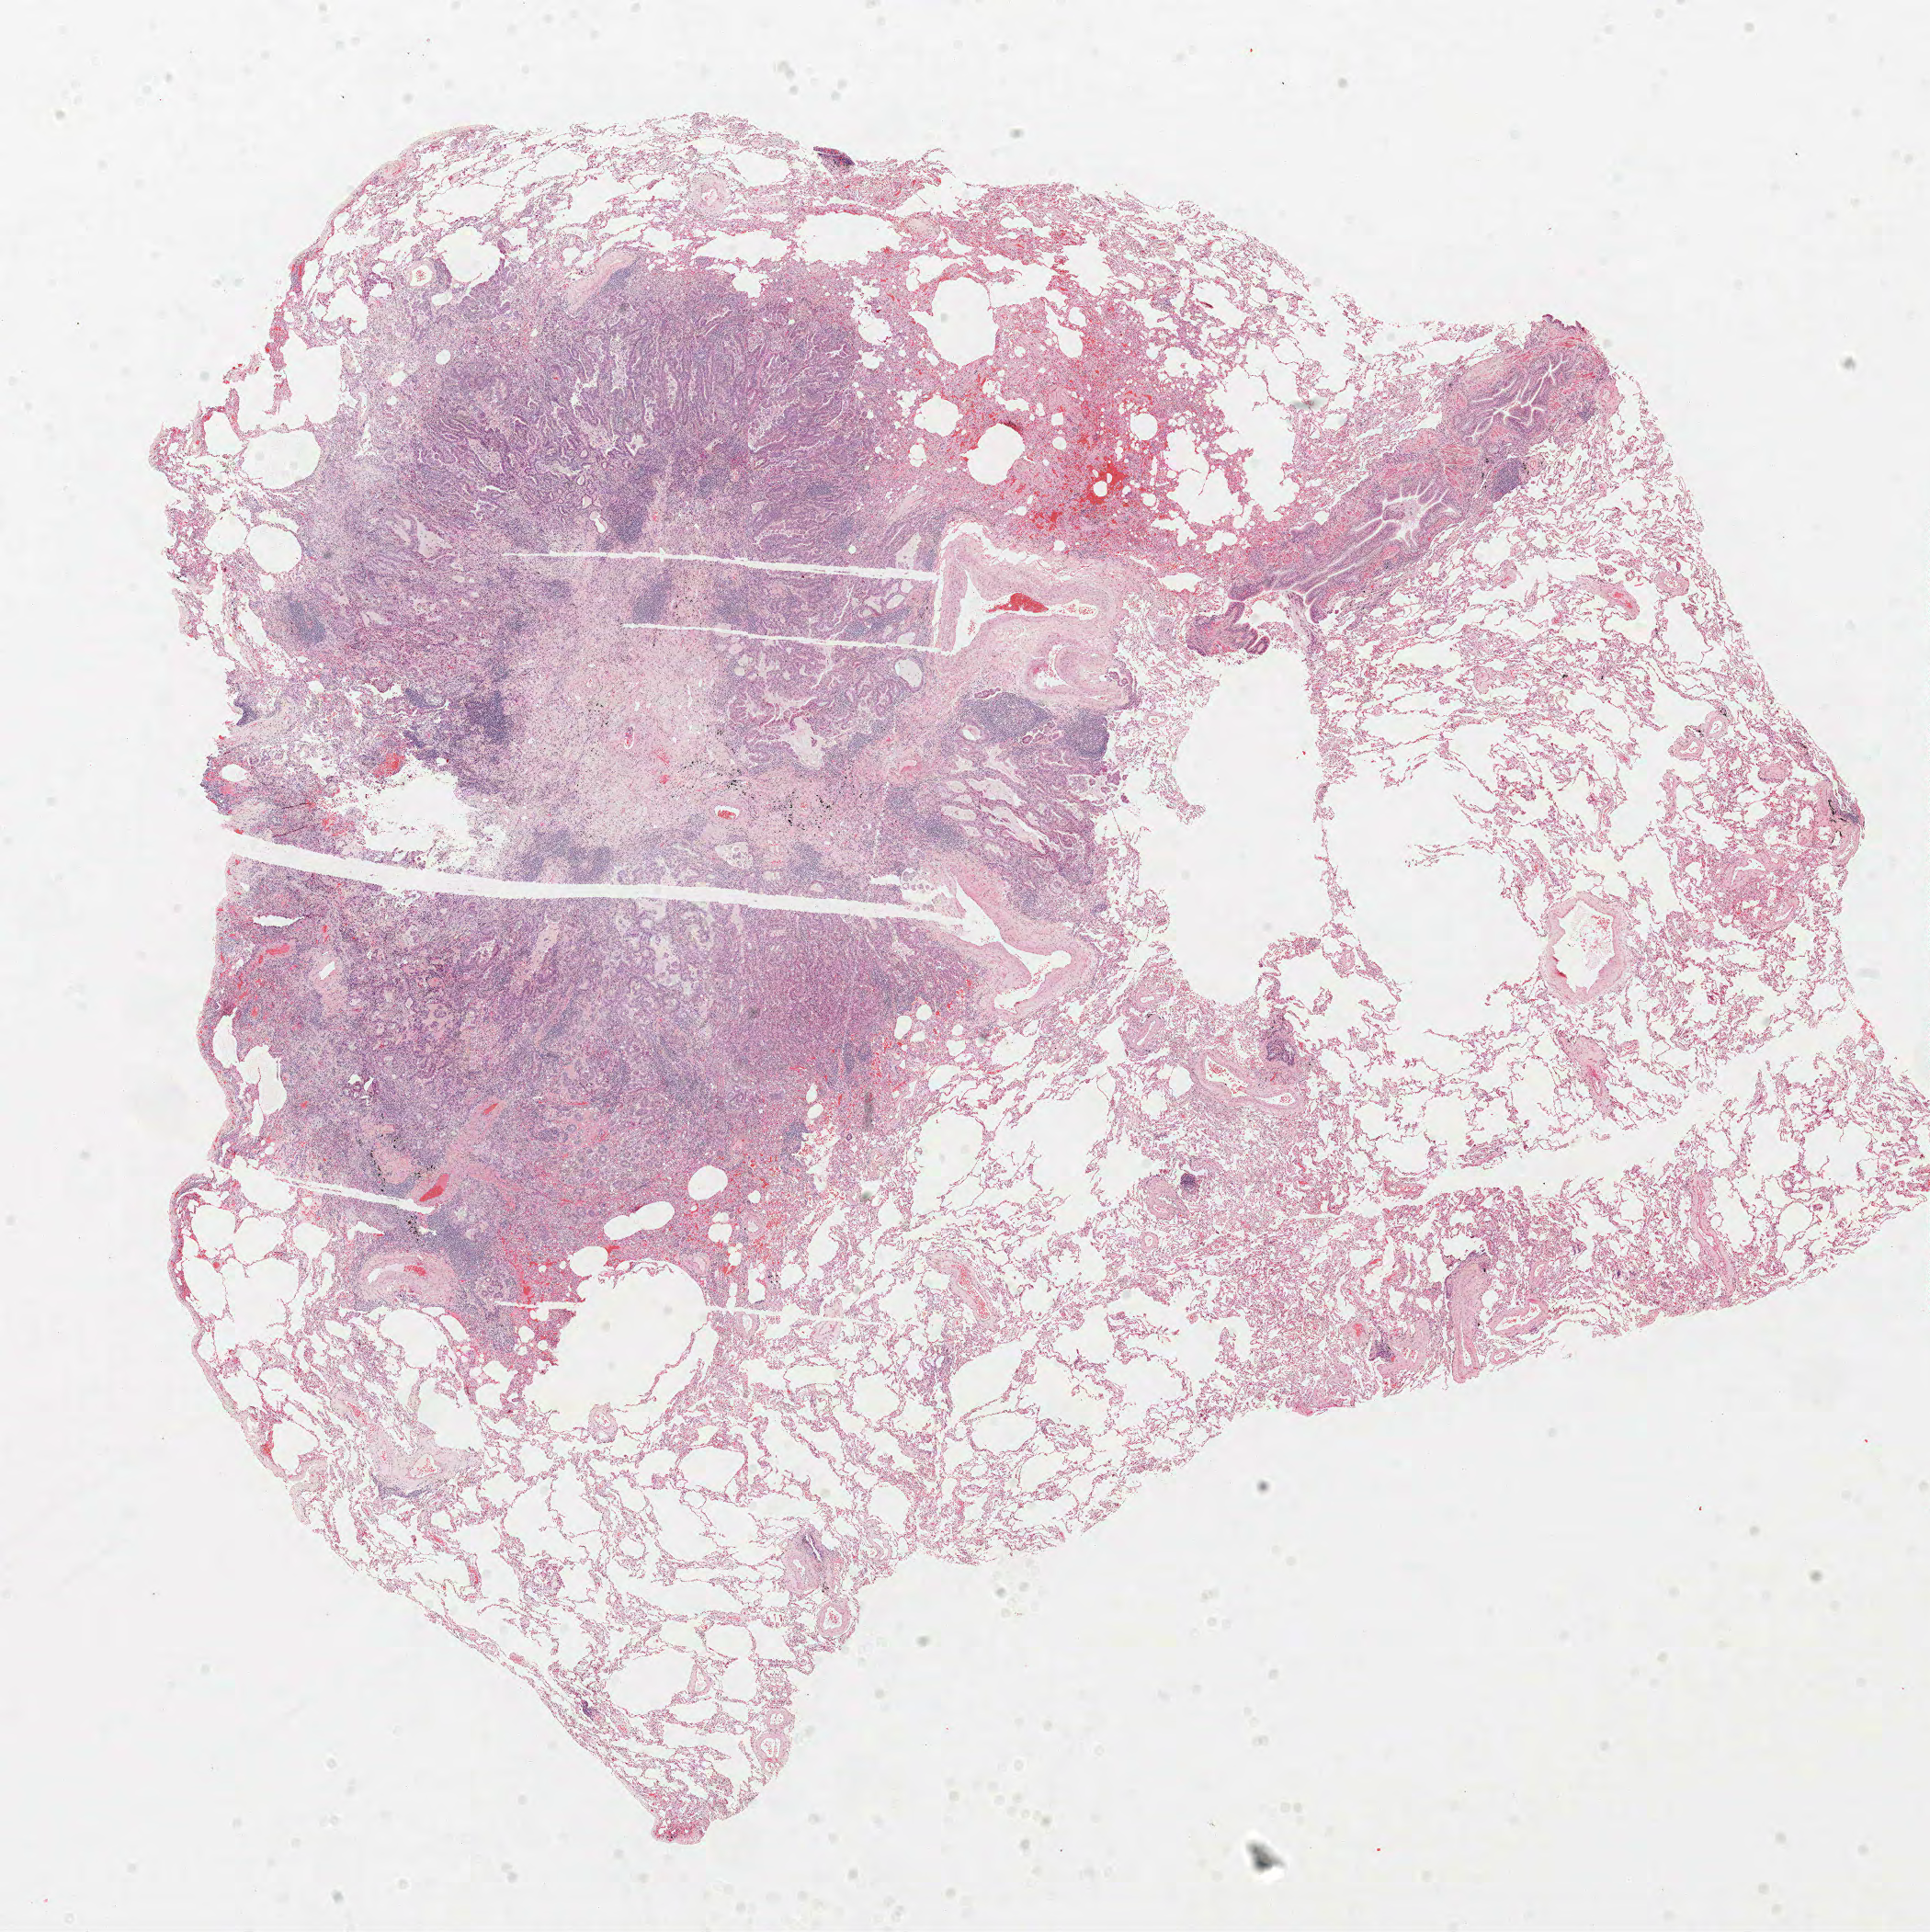
Whole-slide histology image, H&E — low-resolution overview of the scanned area, about 16.8 x 16.8 mm, FFPE section, lung tissue. Female, age 66 at enrolment. Current smoker at enrolment. Grade: moderately differentiated (G2).
Primary tumour location (clinical record): right lower lobe. Stage (AJCC 6th edition): IIA. ICD-O-3 topography: lower lobe of lung (C34.3). Tumour size (pathology): 11 mm. Participant's lung-cancer diagnosis: Adenocarcinoma, NOS (ICD-O-3 8140/3).